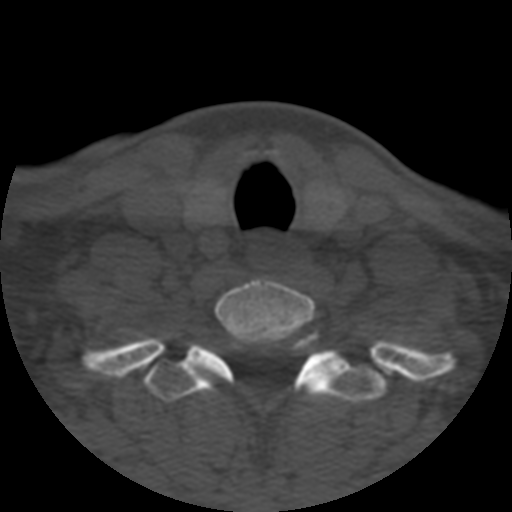
CT including the spine, one axial slice. Slice 455 of 508 in the series (ordered by position). Reconstruction kernel STANDARD. 120 kVp. Bone window (W 1800 / L 400 HU). 512 × 512 image matrix, field of view 160 × 160 mm. Patient age 57 years. Case-level facts recorded for this patient, not image findings: primary cancer: prostate.
Annotated regions visible in this slice (semi-automatic segmentation, software-assisted and operator-edited):
- T1 vertebra: bounding box <104,334,387,403> (left, top, right, bottom; pixels)